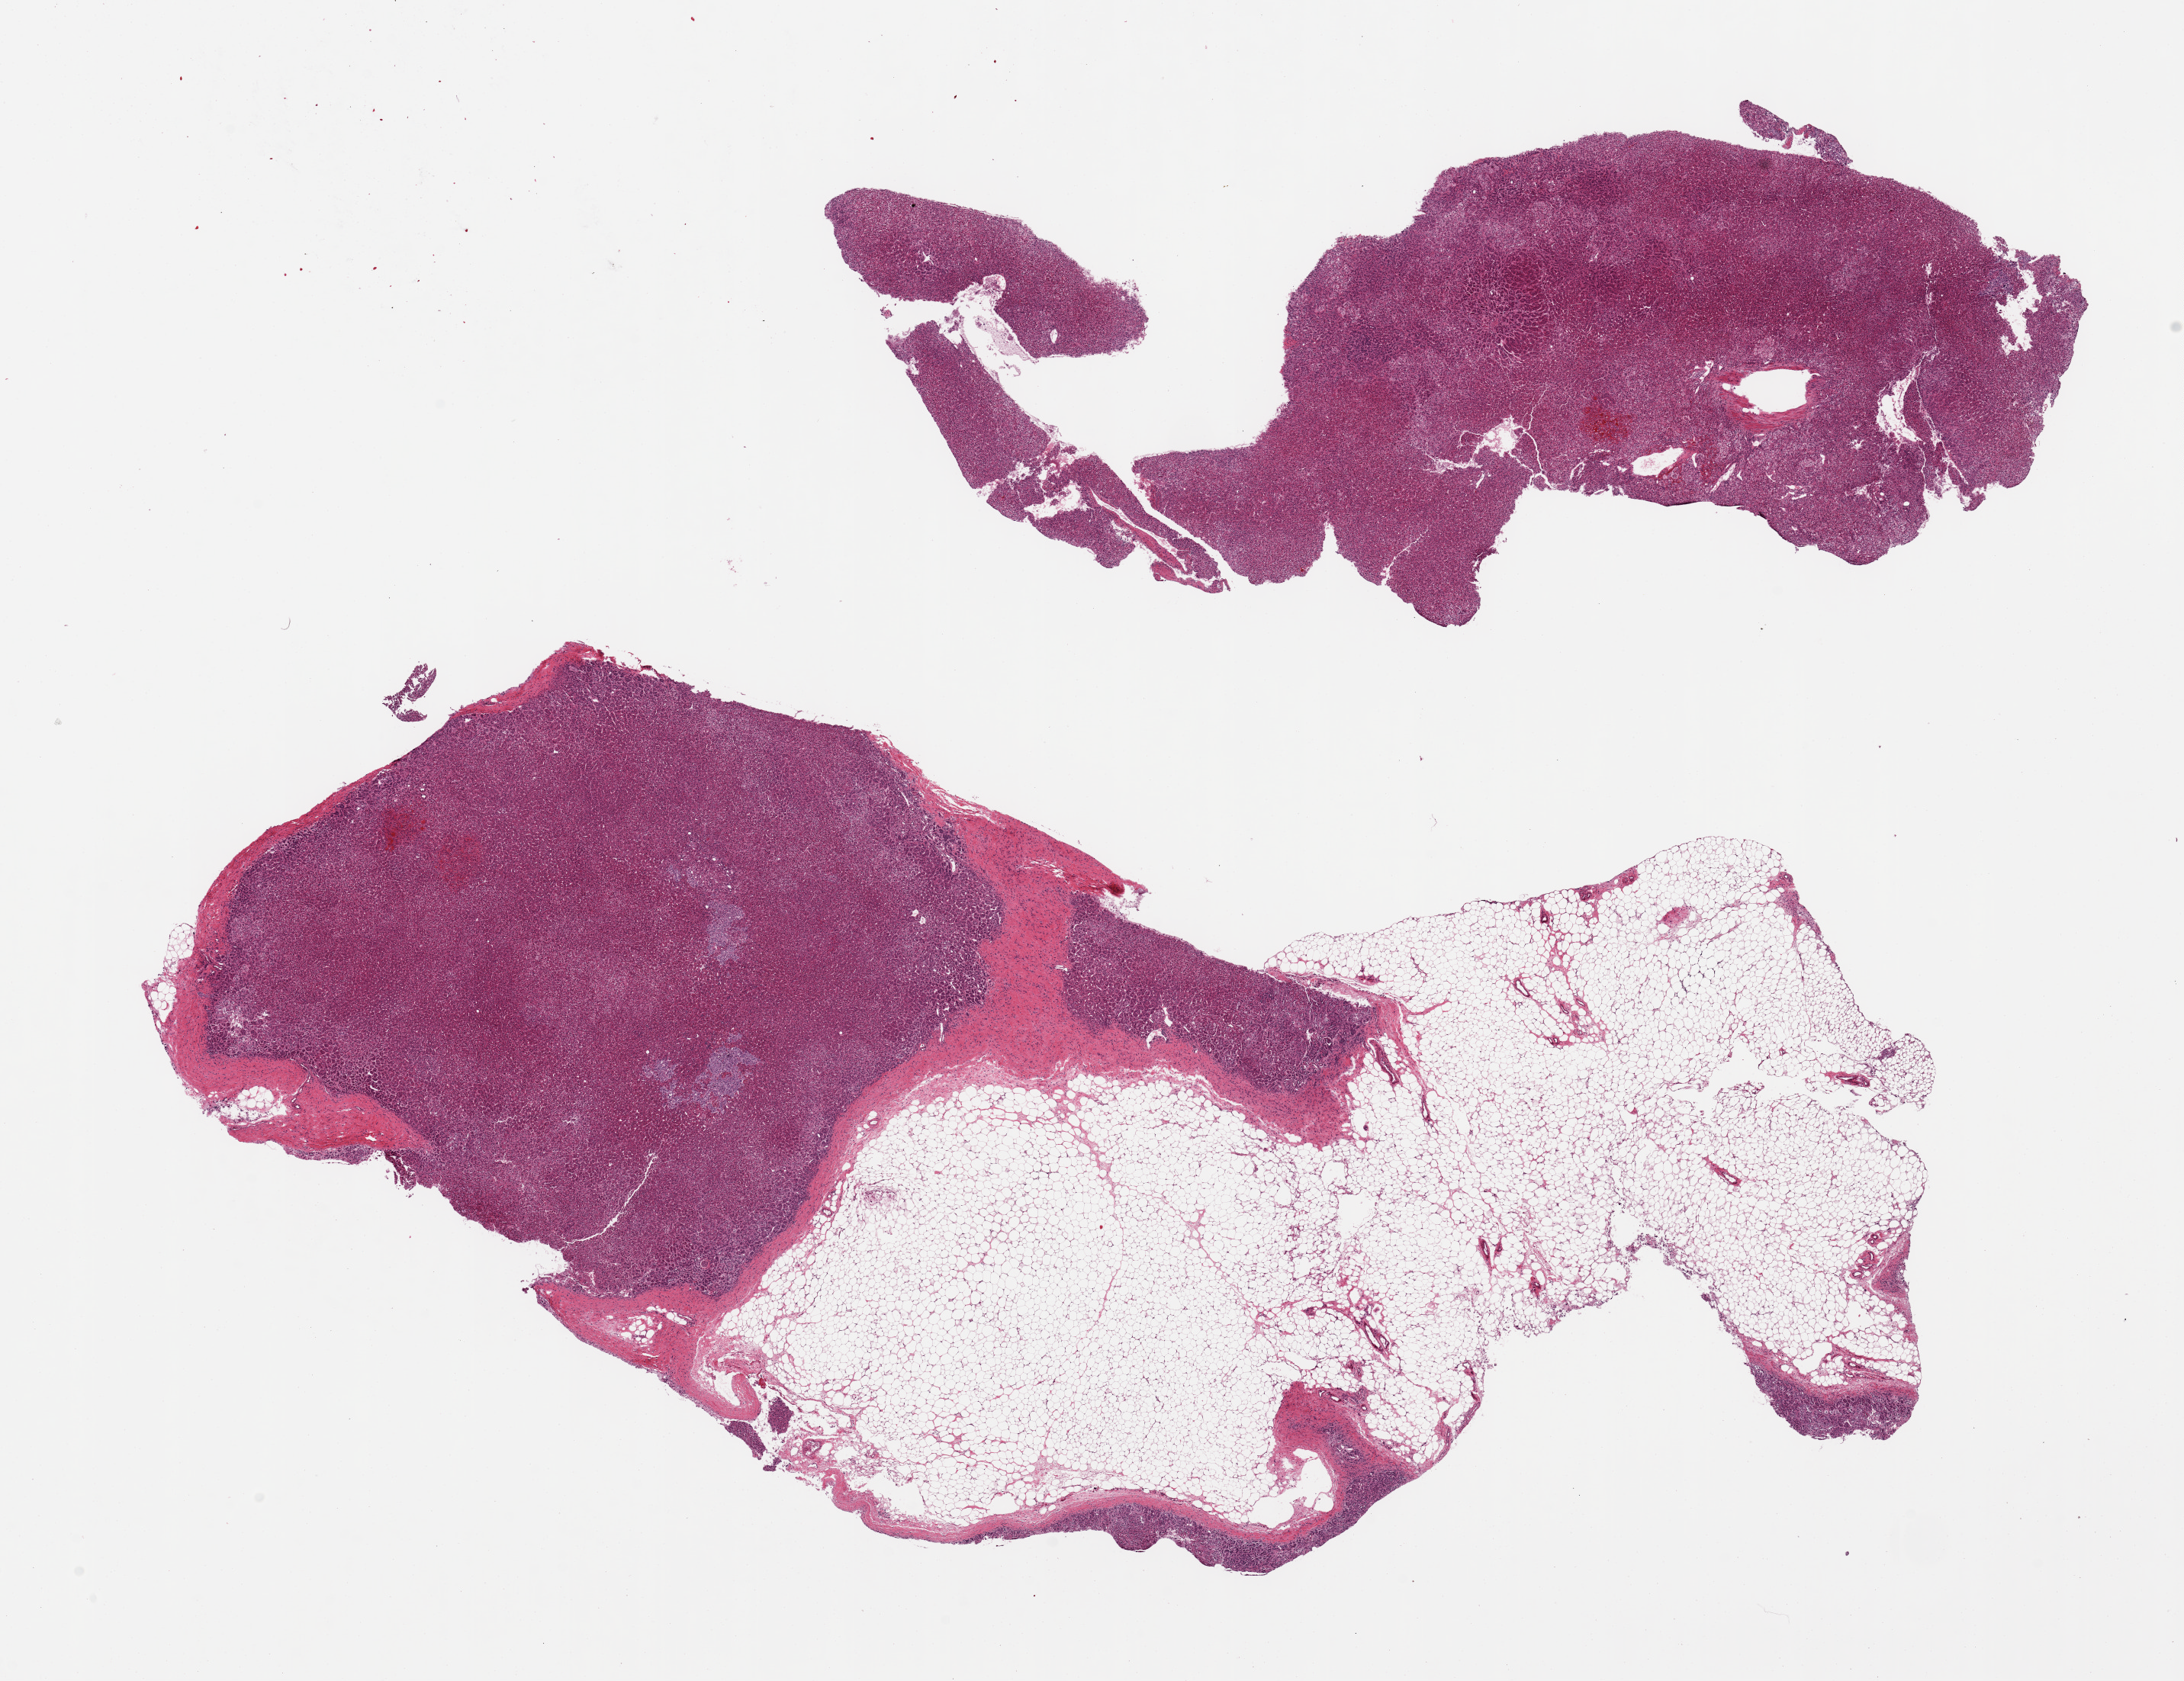
Digitized haematoxylin and eosin-stained section, whole scanned area (about 22.6 x 17.4 mm) shown as a low-resolution overview; PAXgene-fixed paraffin-embedded (PFPE) section; section of adrenal gland (target tissue); donor tissue sample. Donor sex: male.
Pathologist's review note for this sample: 2 pieces, one ~50% attached adipose tissue.